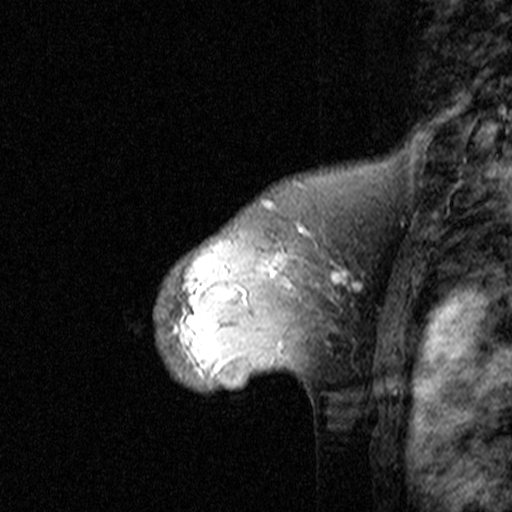
Breast MRI (dynamic contrast-enhanced), one sagittal slice; slice 32 of 44 in the series (ordered by position); dynamic contrast-enhanced study with each time point stored as its own series, time point 2 of 3 at this slice position (early post-contrast, ordered by acquisition time); 1.5 T; TE 4.5 ms, TR 11 ms; 512 × 512 image matrix. Female patient, age 46 years. Case-level facts recorded for this patient, not image findings: setting: breast cancer imaged before/during neoadjuvant chemotherapy; receptor status: HER2-positive.
Outlined on this slice (semi-automatically segmented with operator editing):
- analysis volume of interest (the breast-tissue region the enhancement analysis was run in; not a lesion): bounding box (x1, y1, x2, y2) in pixels: (144, 172, 359, 393)
- tumour enhancement mask (voxels above the 90 % enhancement threshold inside the analysis volume of interest): (187, 205, 350, 346)